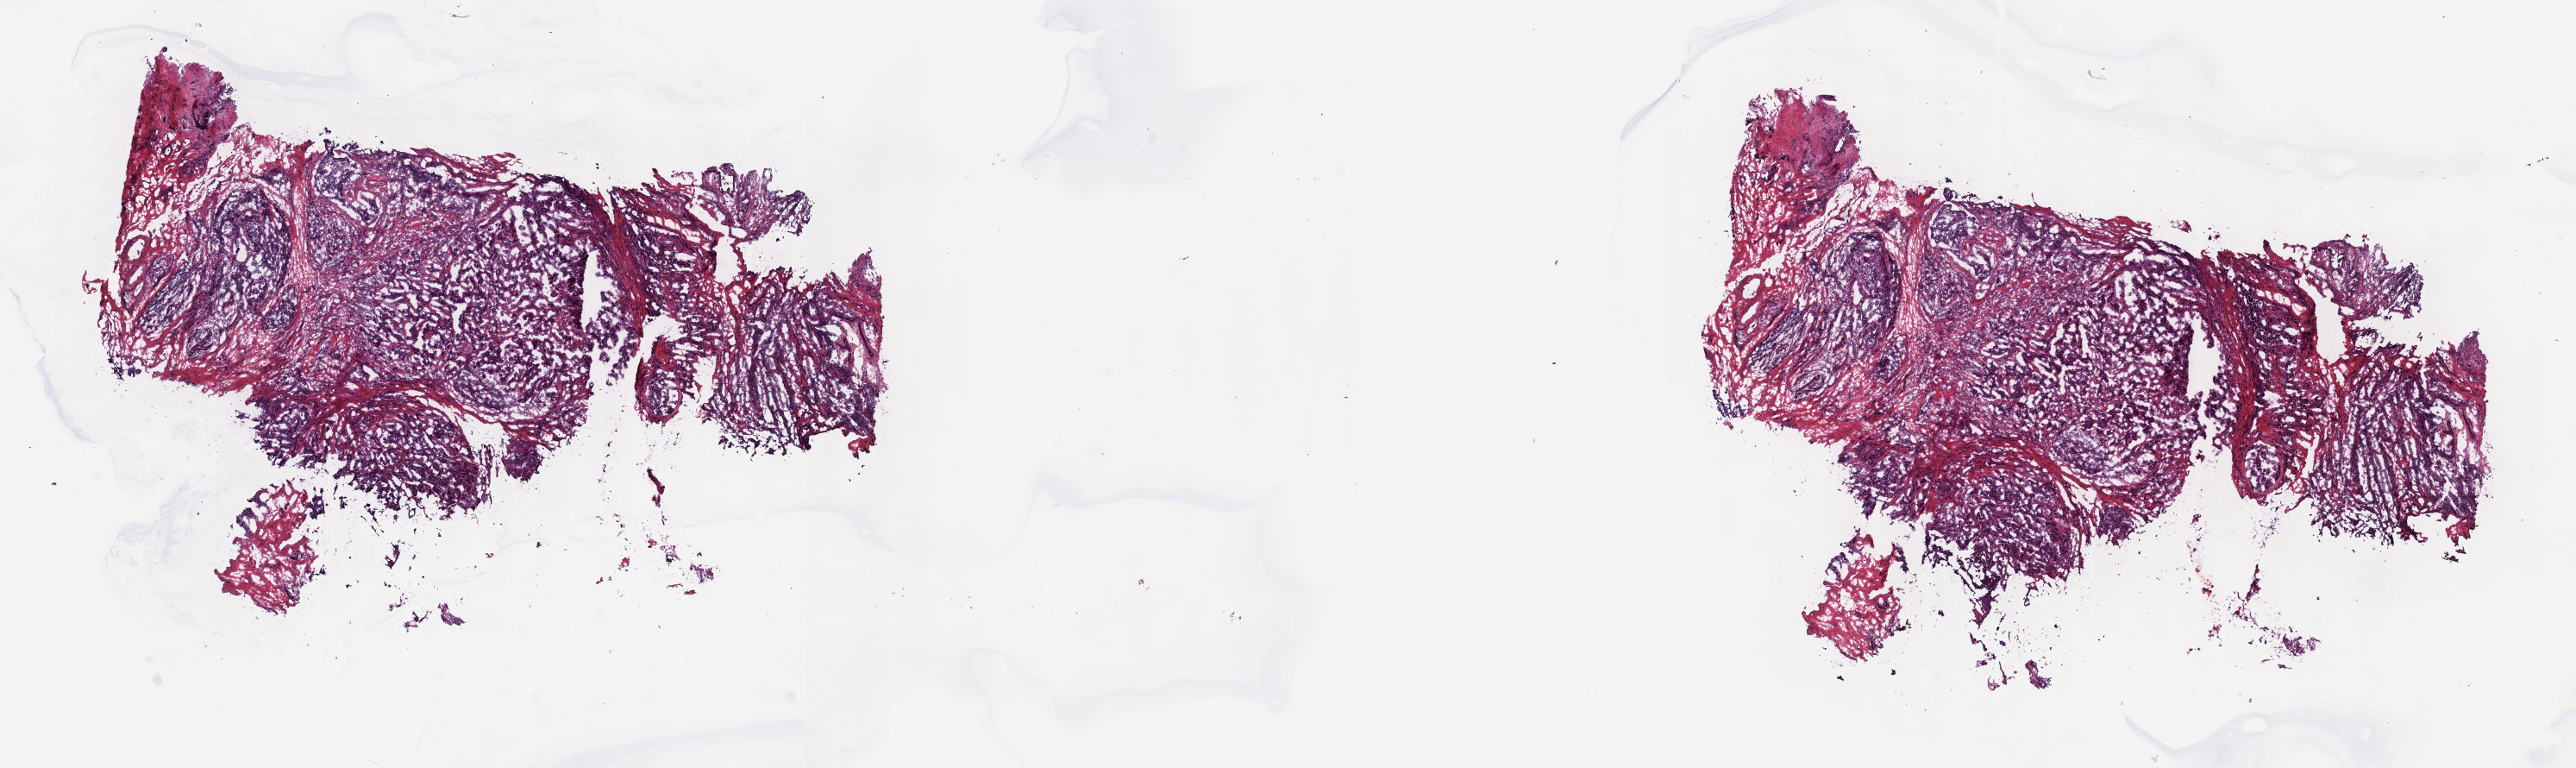
Digitized Hematoxylin and eosin (H&E) stained tissue section (whole slide), low-resolution overview of the scanned area, about 24.2 x 7.2 mm (acquisition: 40x scan). Formalin-fixed paraffin-embedded (FFPE) diagnostic section. Sample: primary tumour, breast. Patient: female, age at initial diagnosis 54 years.
AJCC pathologic stage: IIIB (7th edition). TNM: T4 N0 M0. Diagnosis: Medullary carcinoma, NOS.